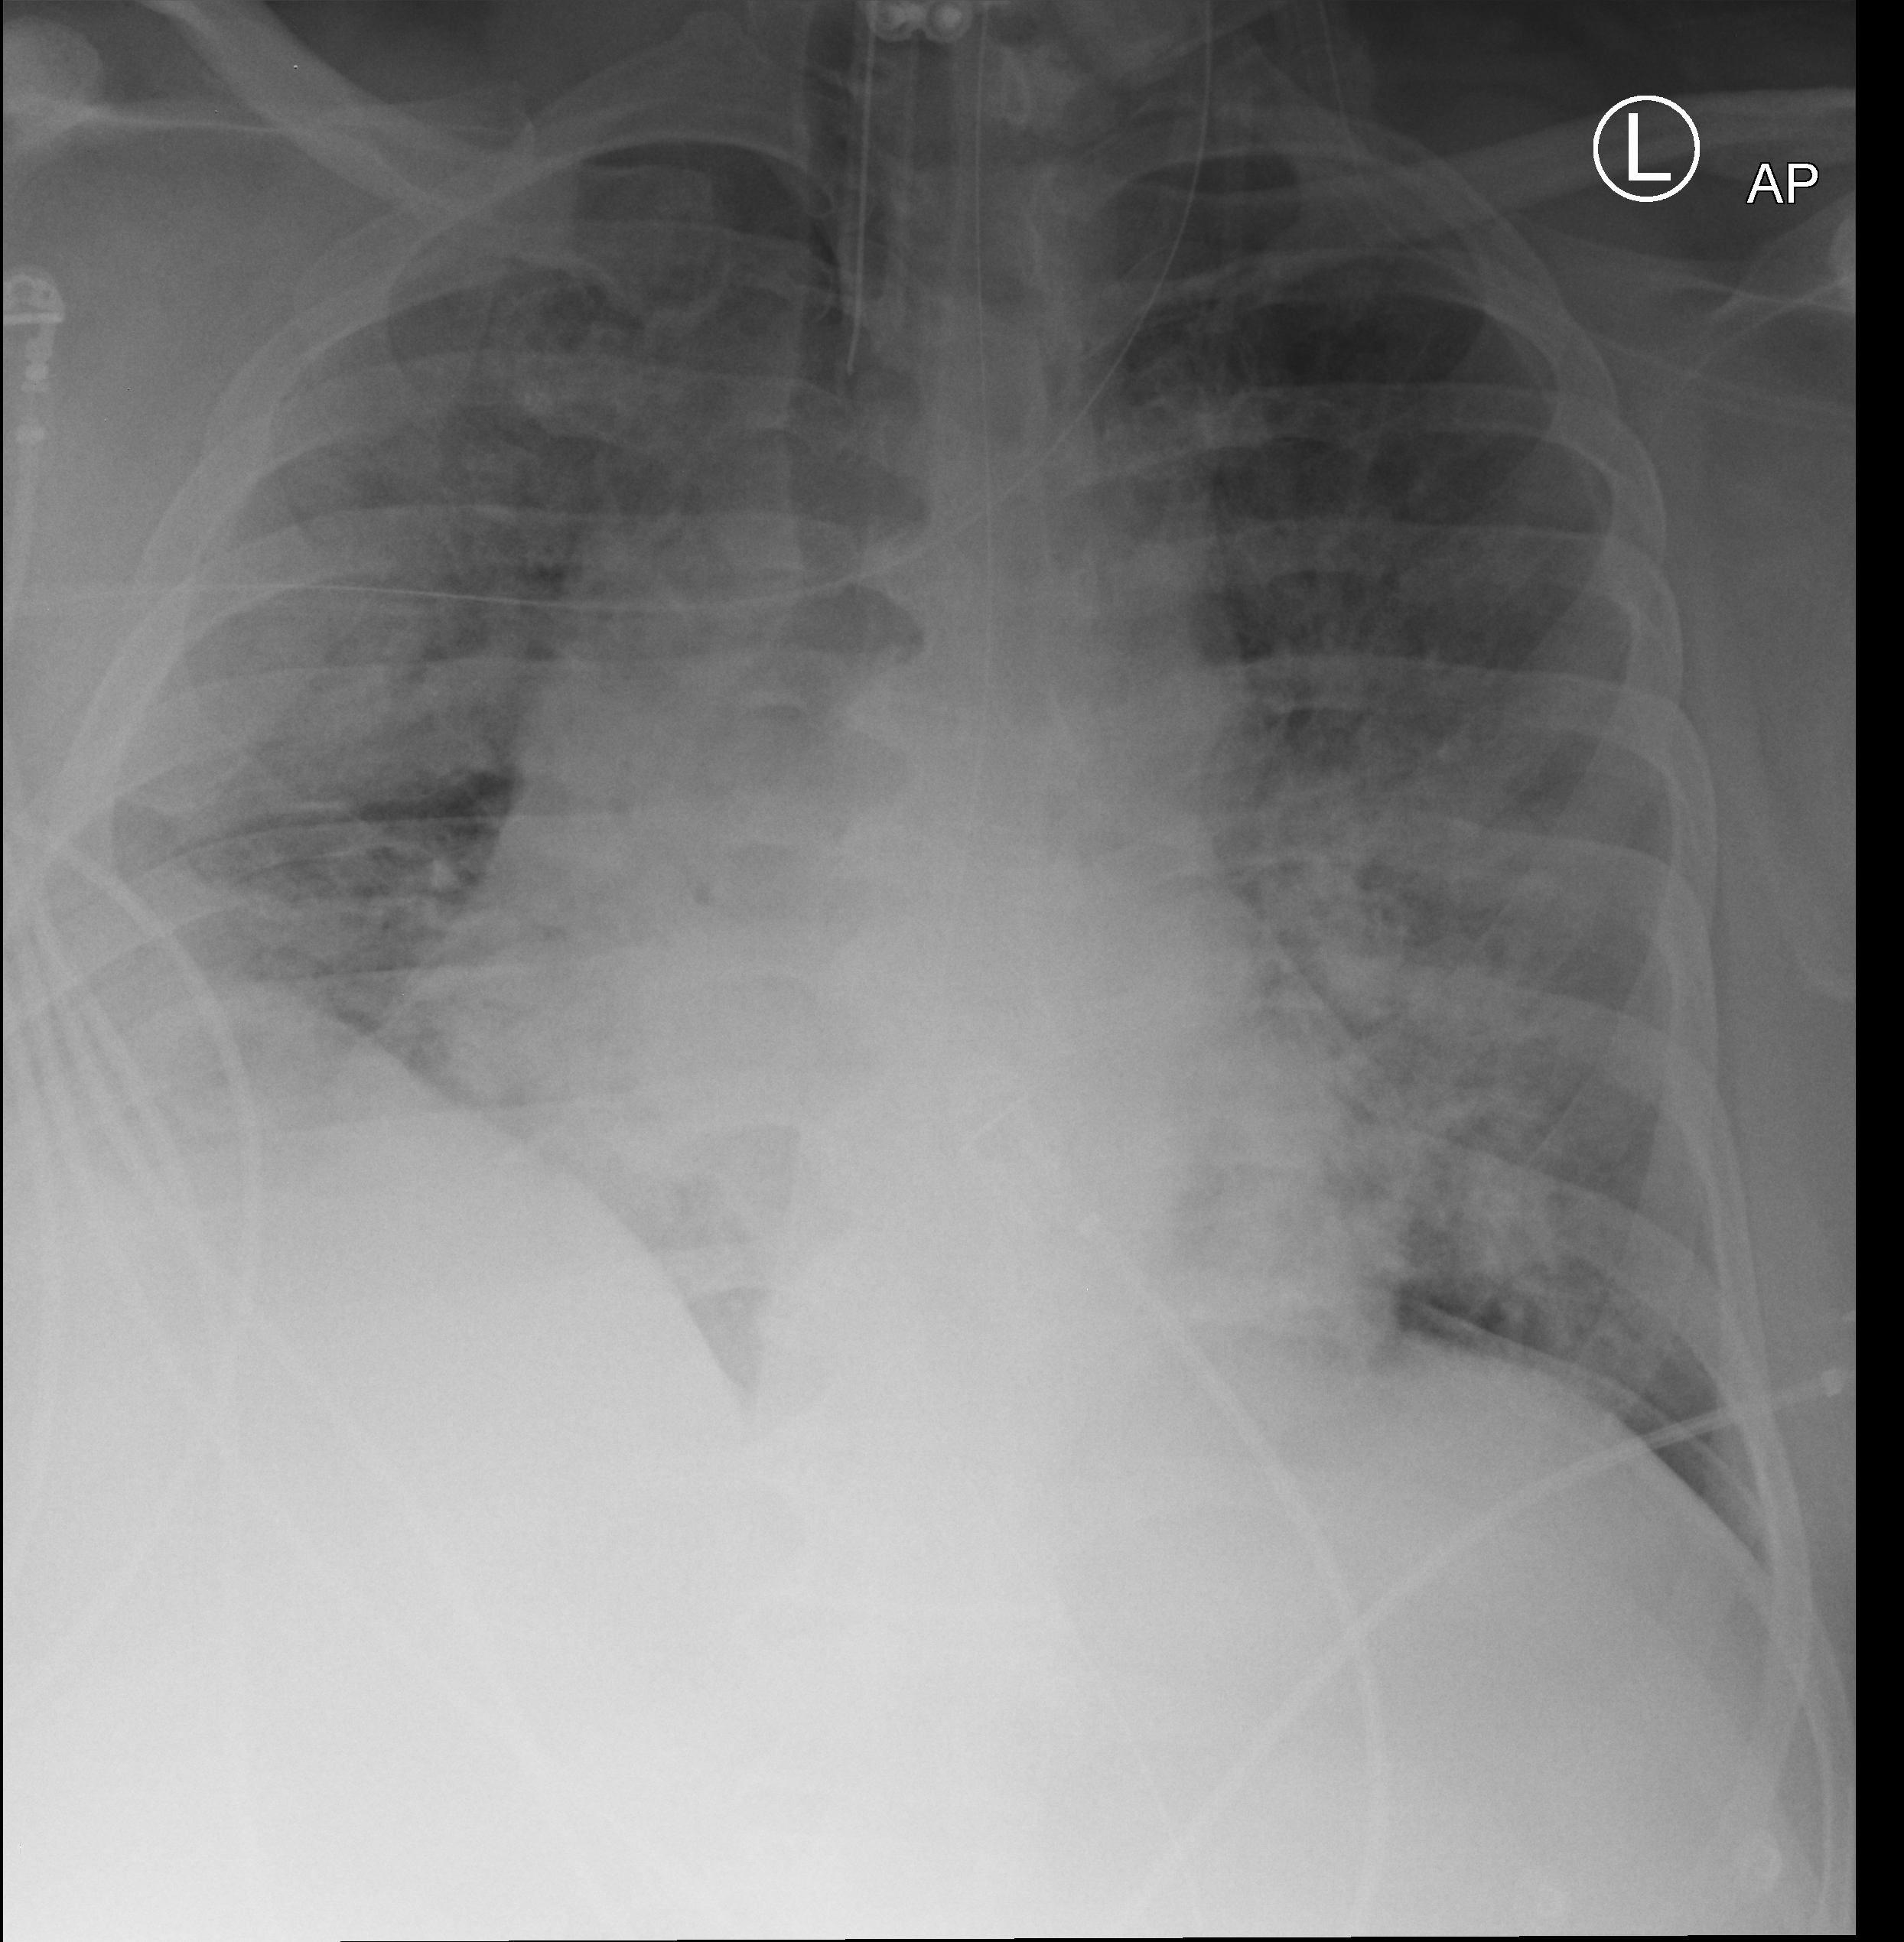
Portable chest radiograph, anteroposterior (AP) projection. Male patient hospitalised with COVID-19, age 18–59 years.
From the hospital-stay record, not from the radiograph (when in the stay this image was taken is not recorded): admitted to intensive care during this hospital stay: yes; chronic kidney disease (admission record): no.